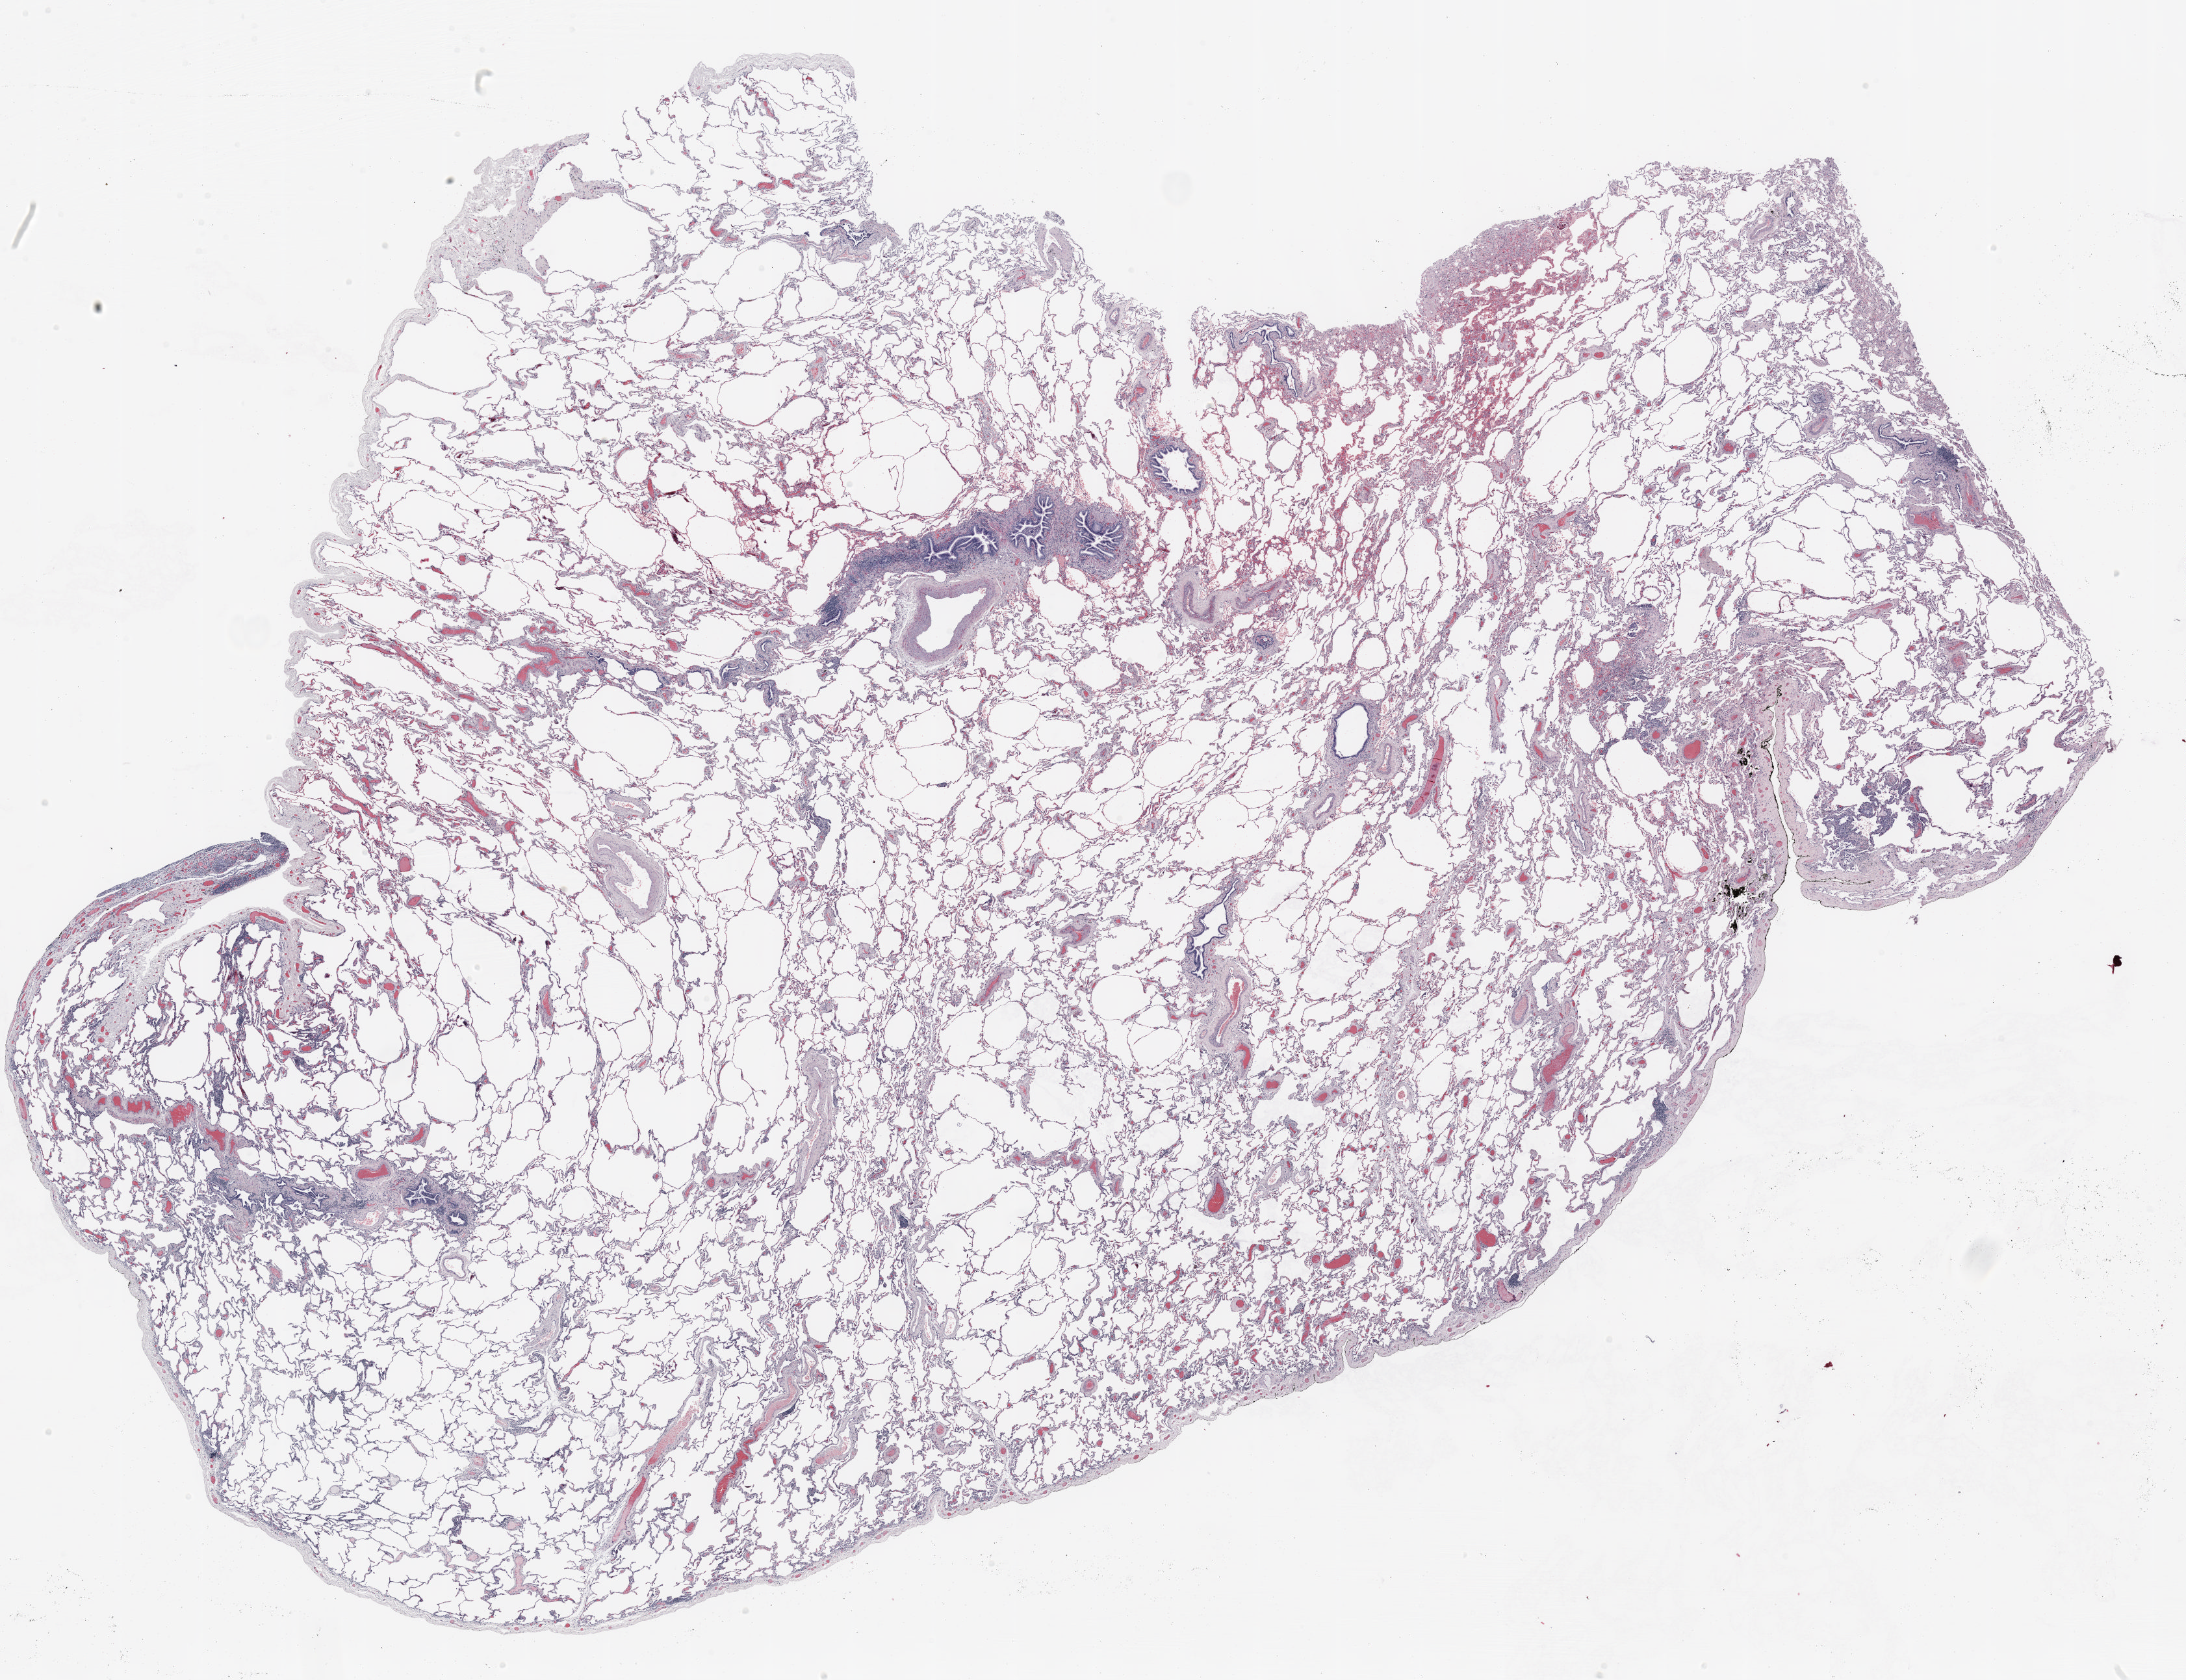
Hematoxylin and eosin (H&E) stained whole-slide image — whole scanned area (about 27.0 x 20.8 mm) shown as a low-resolution overview, FFPE section, lung. Female, age 66 at enrolment. Former smoker at enrolment. Grade: moderately differentiated (G2).
Stage (AJCC 6th edition): IA. Primary tumour location (clinical record): right middle lobe. Participant's lung-cancer diagnosis: Adenocarcinoma, NOS. Tumour size (pathology): 11 mm.